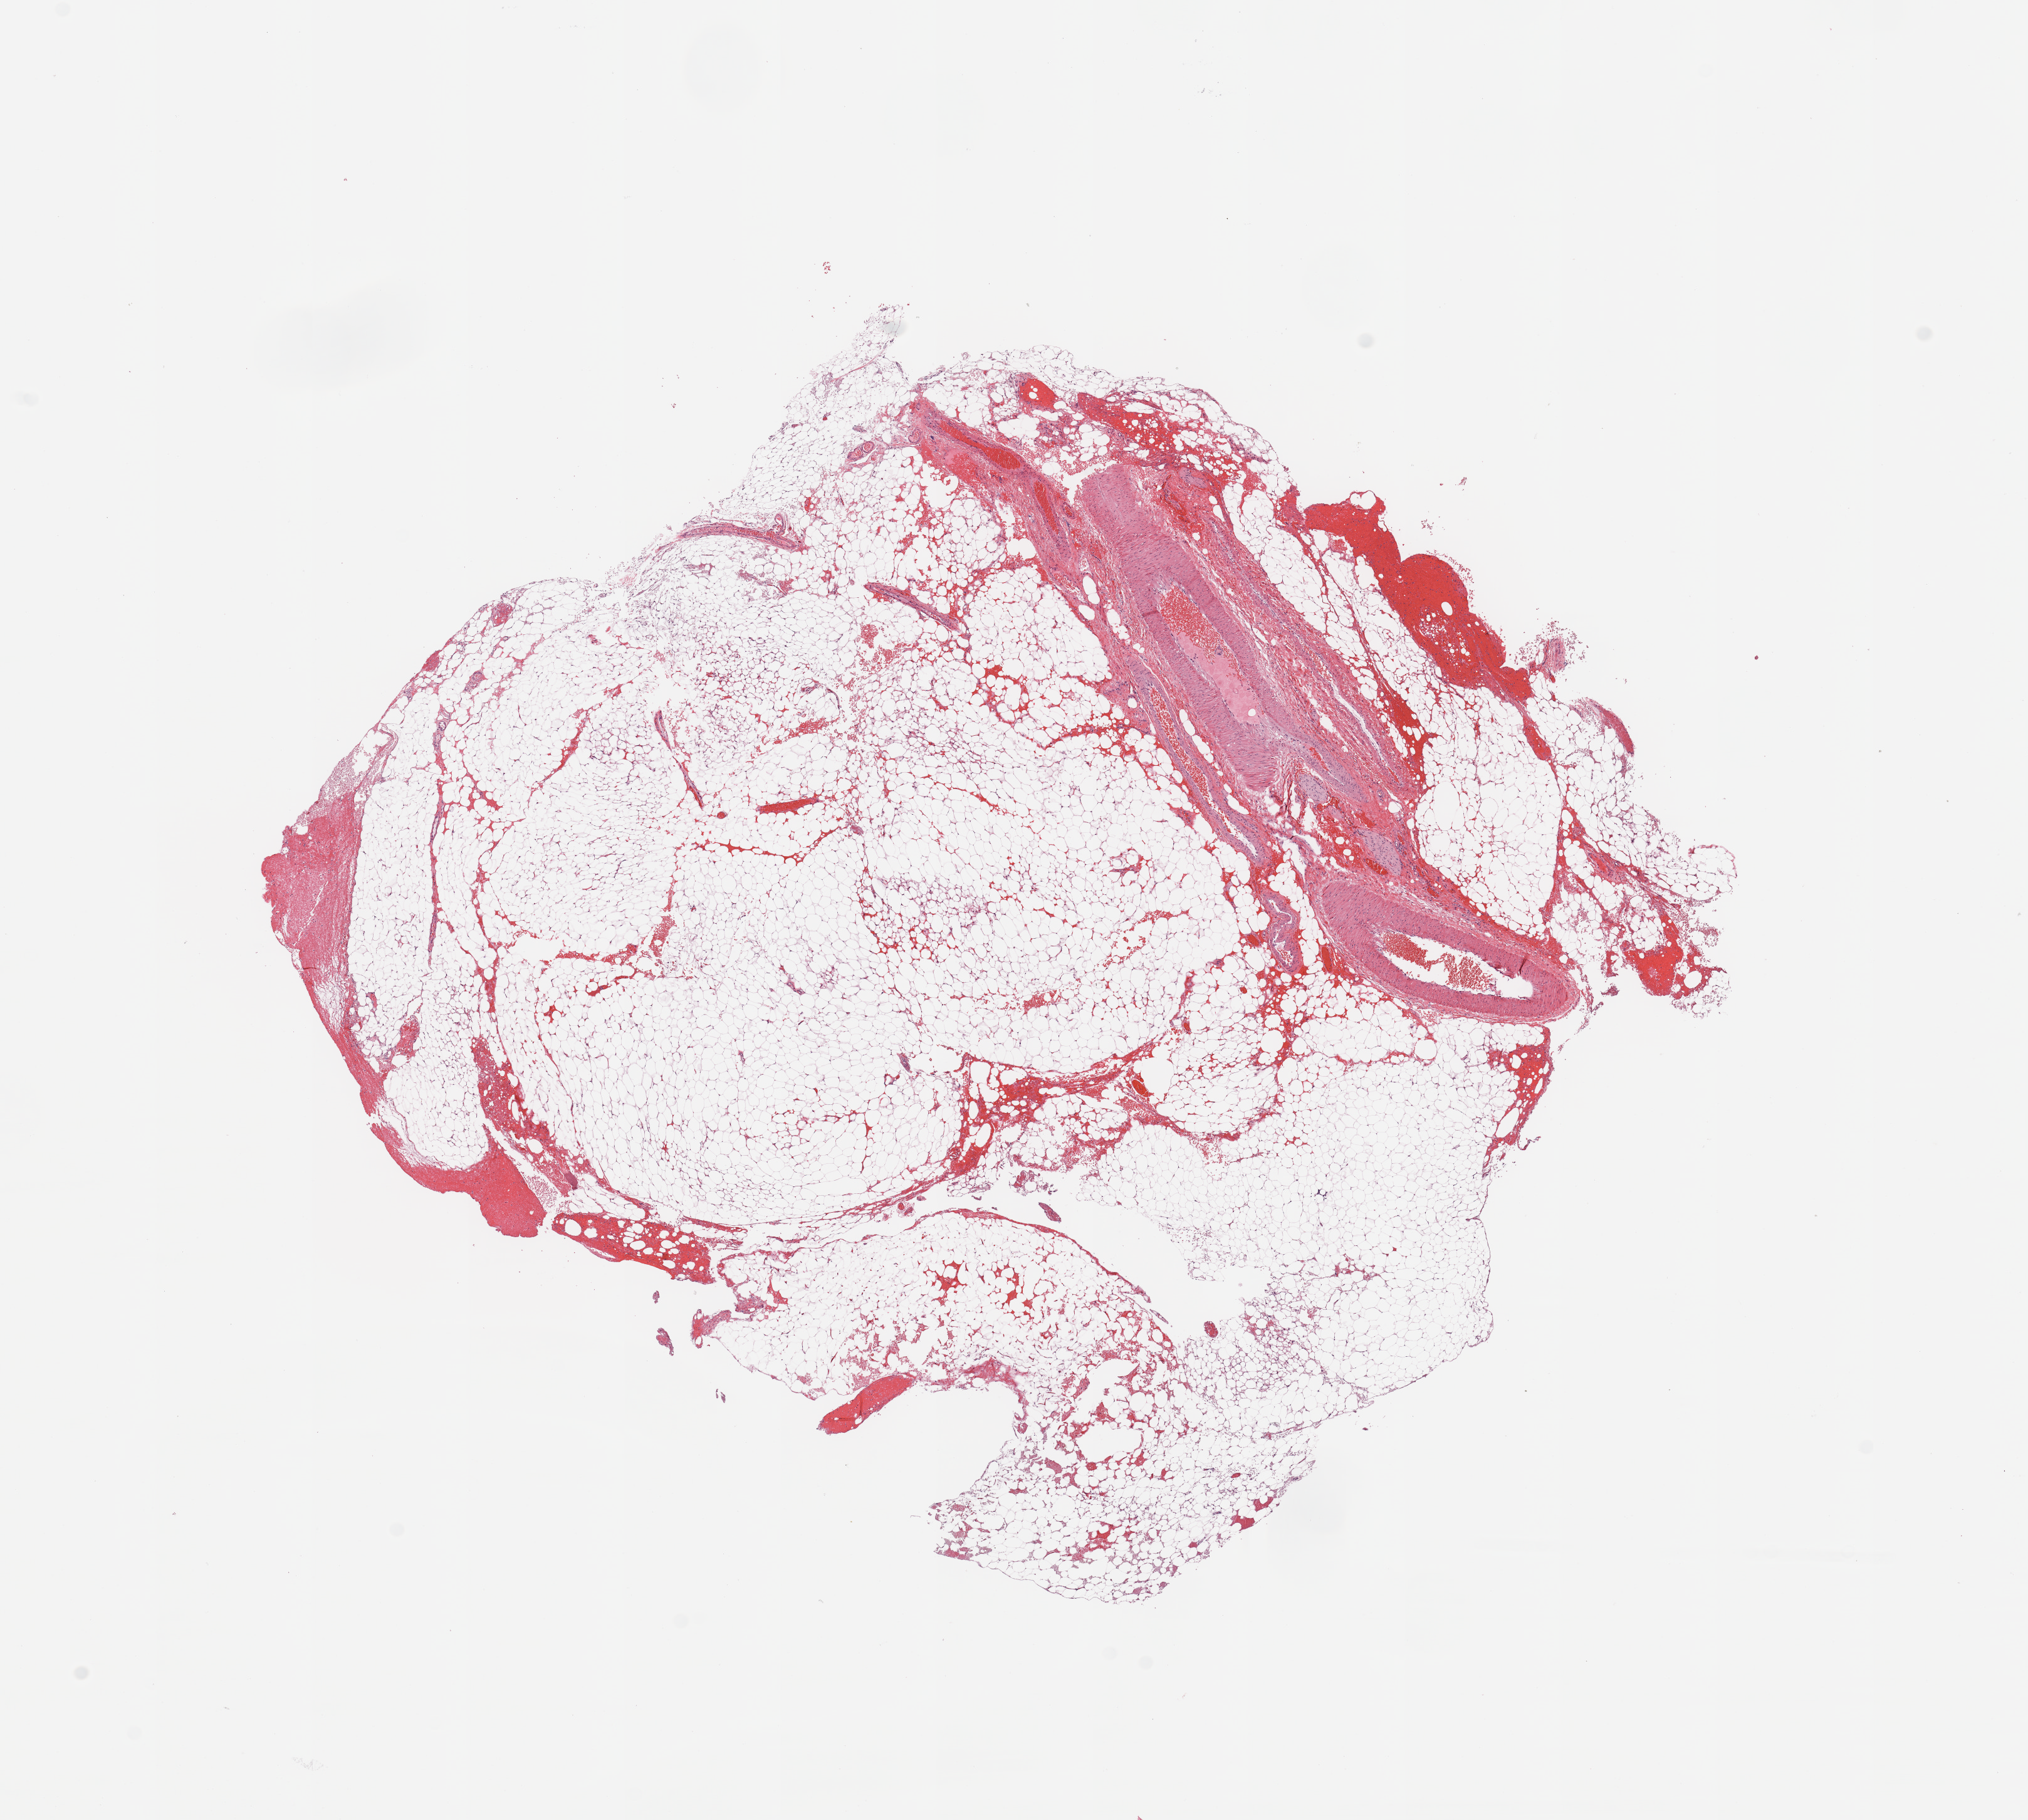
H&E-stained whole-slide image — a low-resolution overview of the entire scanned area, about 12.8 x 11.5 mm (from a 20x scan). Kidney, normal (non-tumour) tissue. 48-year-old female patient.
This section: normal (non-tumour) tissue from the same patient. Patient diagnosis: Renal cell carcinoma, NOS.